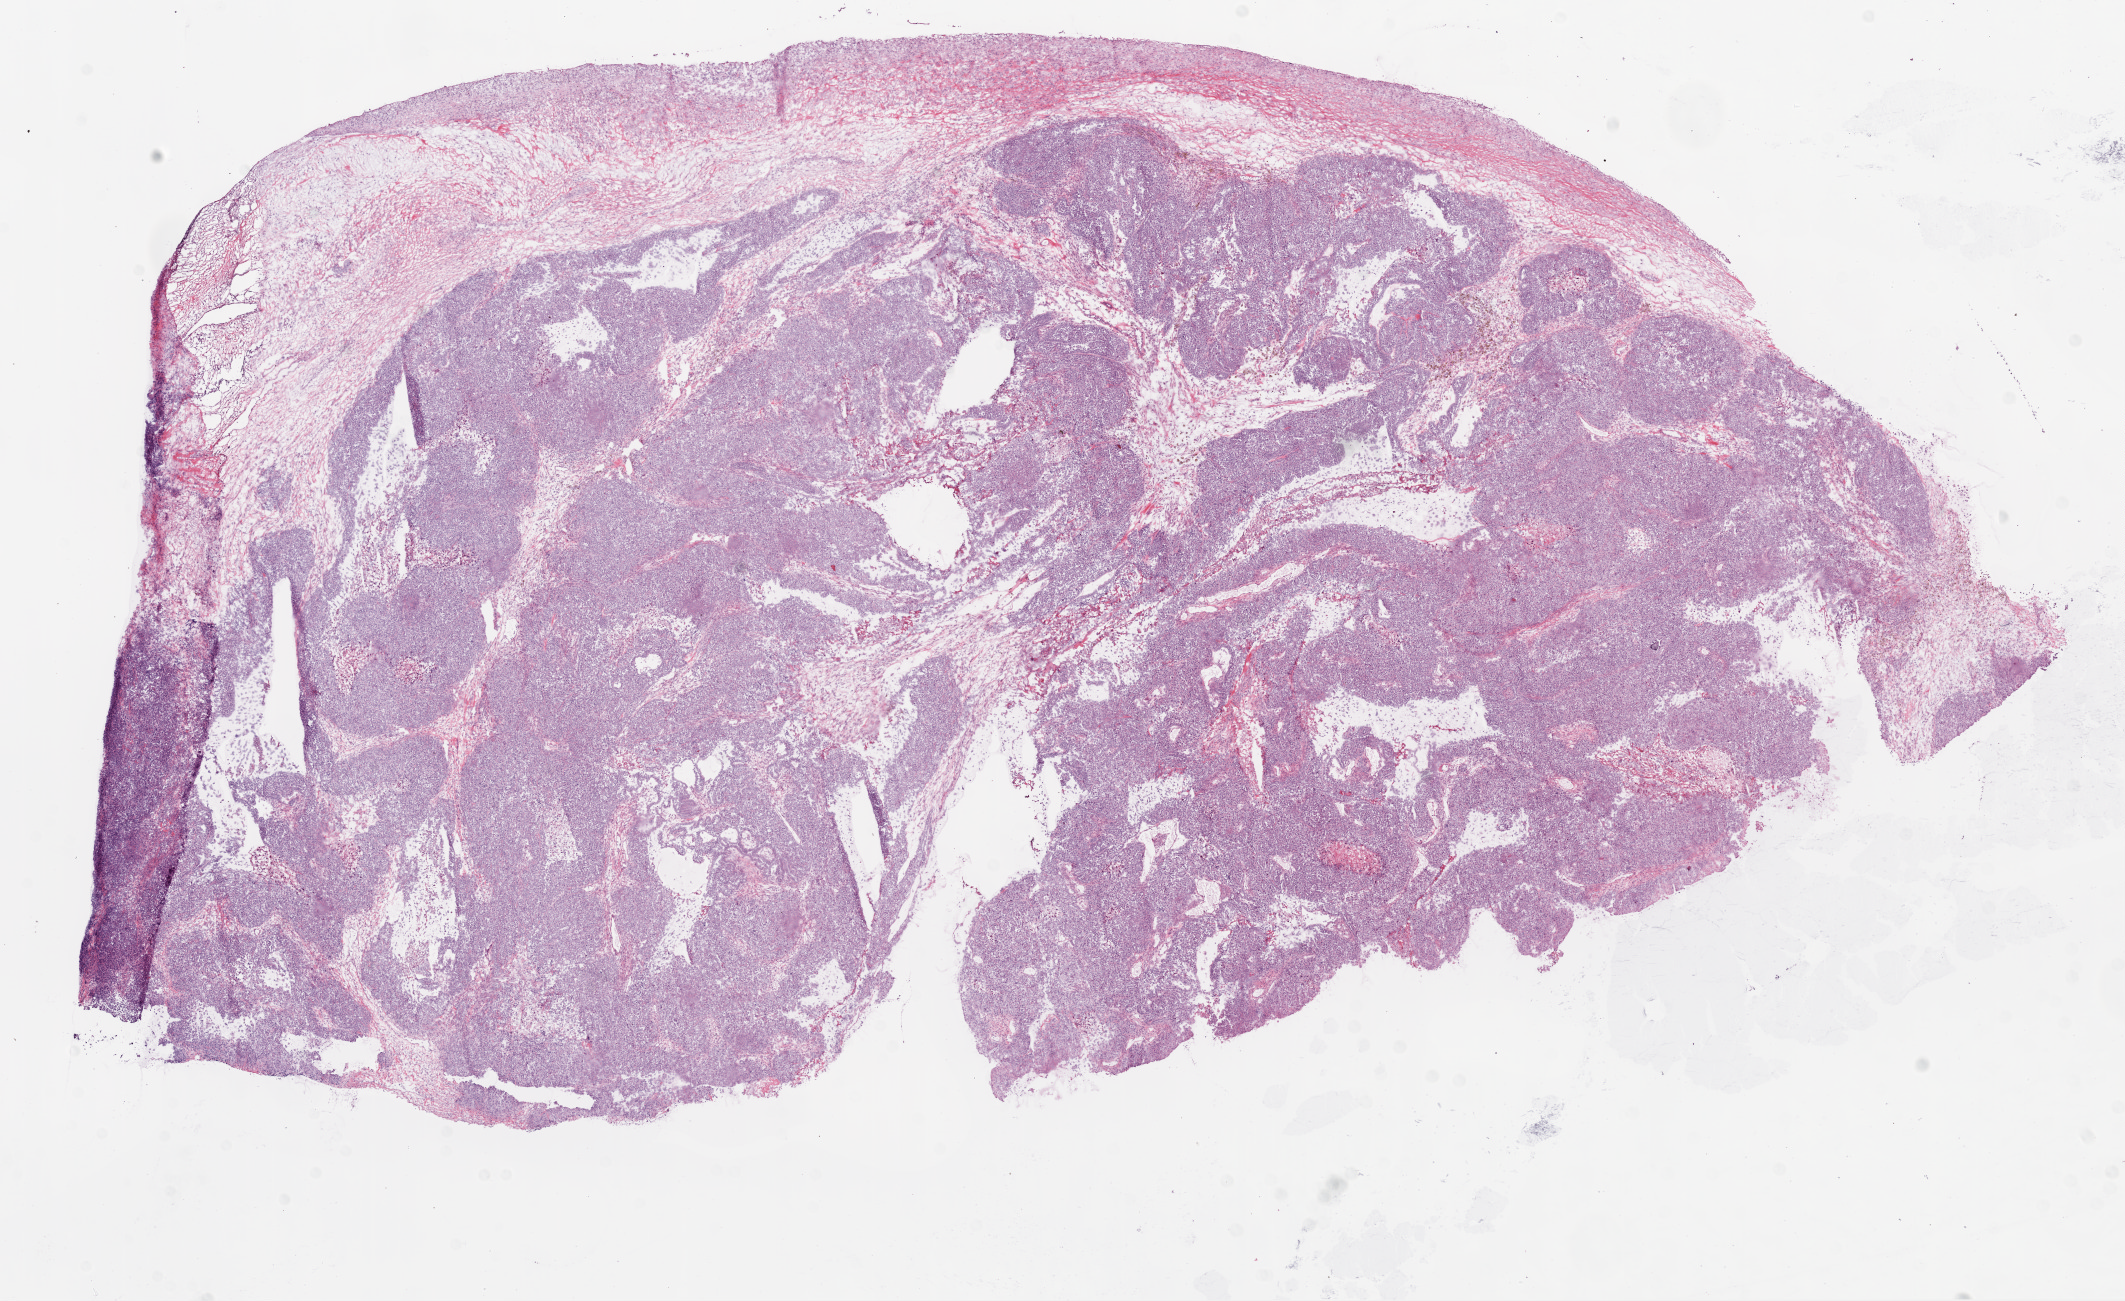
Whole-slide histology image, H&E-stained — whole scanned area (about 17.1 x 10.4 mm, from a 20x scan) shown as a low-resolution overview, frozen section from the top of the tissue portion, ovary, primary tumour sample. Female, age 60 years at initial diagnosis. Histologic grade: G3 (poorly differentiated). Pathologist review of this section (percent, as recorded): tumour cells 80%, tumour nuclei 90%, normal cells 0%, stromal cells 10%, necrosis 10%.
• FIGO stage: IIIB
• pathologic diagnosis: Serous cystadenocarcinoma, NOS